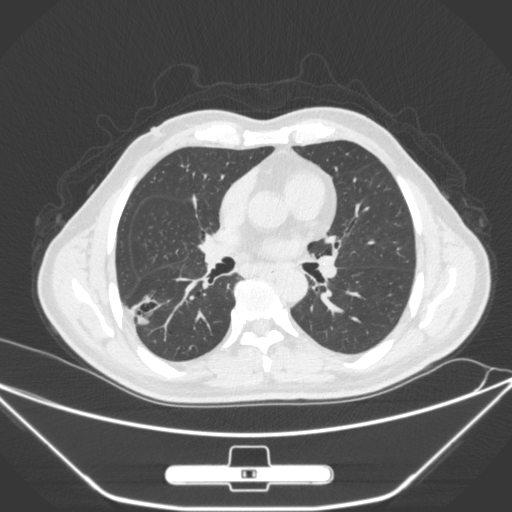
Chest CT, one axial slice. Position 151 of 310 along the scan axis. 120 kVp. Lung window (W 1500 / L -600 HU). 1 mm slice thickness. 512 × 512 image matrix. Male patient, age 71 years. From the clinical record (not read from this slice): clinical TNM (as recorded): T1c N0 M0; histopathological grade: G2.
Annotated regions visible in this slice (rectangle marked by the reading radiologist):
- lung tumour (recorded histology: adenocarcinoma): bounding box (x1, y1, x2, y2) in pixels: (128, 287, 169, 330)